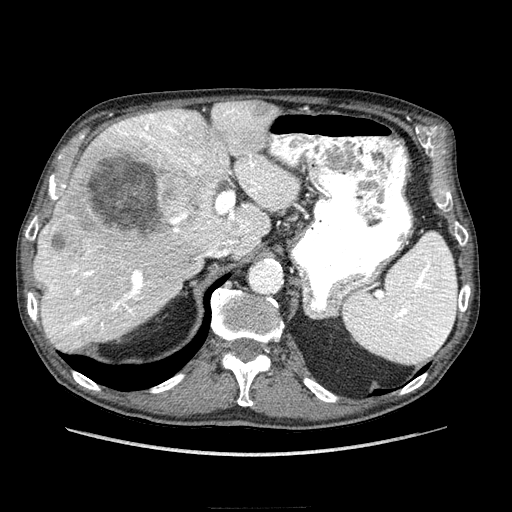
Contrast-enhanced abdominal CT (liver protocol), one axial slice. Slice 159 of 218 in the series (ordered by position). 100 kVp. Soft-tissue window (W 400 / L 40 HU). 2.5 mm slice thickness. 512 × 512 image matrix. Case-level facts recorded for this patient, not image findings: diagnosis: hepatocellular carcinoma (patient treated with transarterial chemoembolisation; whether this scan precedes or follows treatment is not stated here); TNM stage (as recorded): Stage-IIIA; Child-Pugh class: A; tumour nodularity: multinodular; tumour size: 20 cm.
Annotated regions visible in this slice (semi-automatically segmented with operator editing):
- liver parenchyma outside the tumour (the mass and vessels are separate outlines, so this box may not span the whole liver): box from (x=34, y=102) to (x=298, y=350) px
- mass: (x=47, y=109)–(x=229, y=258)
- liver vessels: (x=38, y=108)–(x=297, y=334)